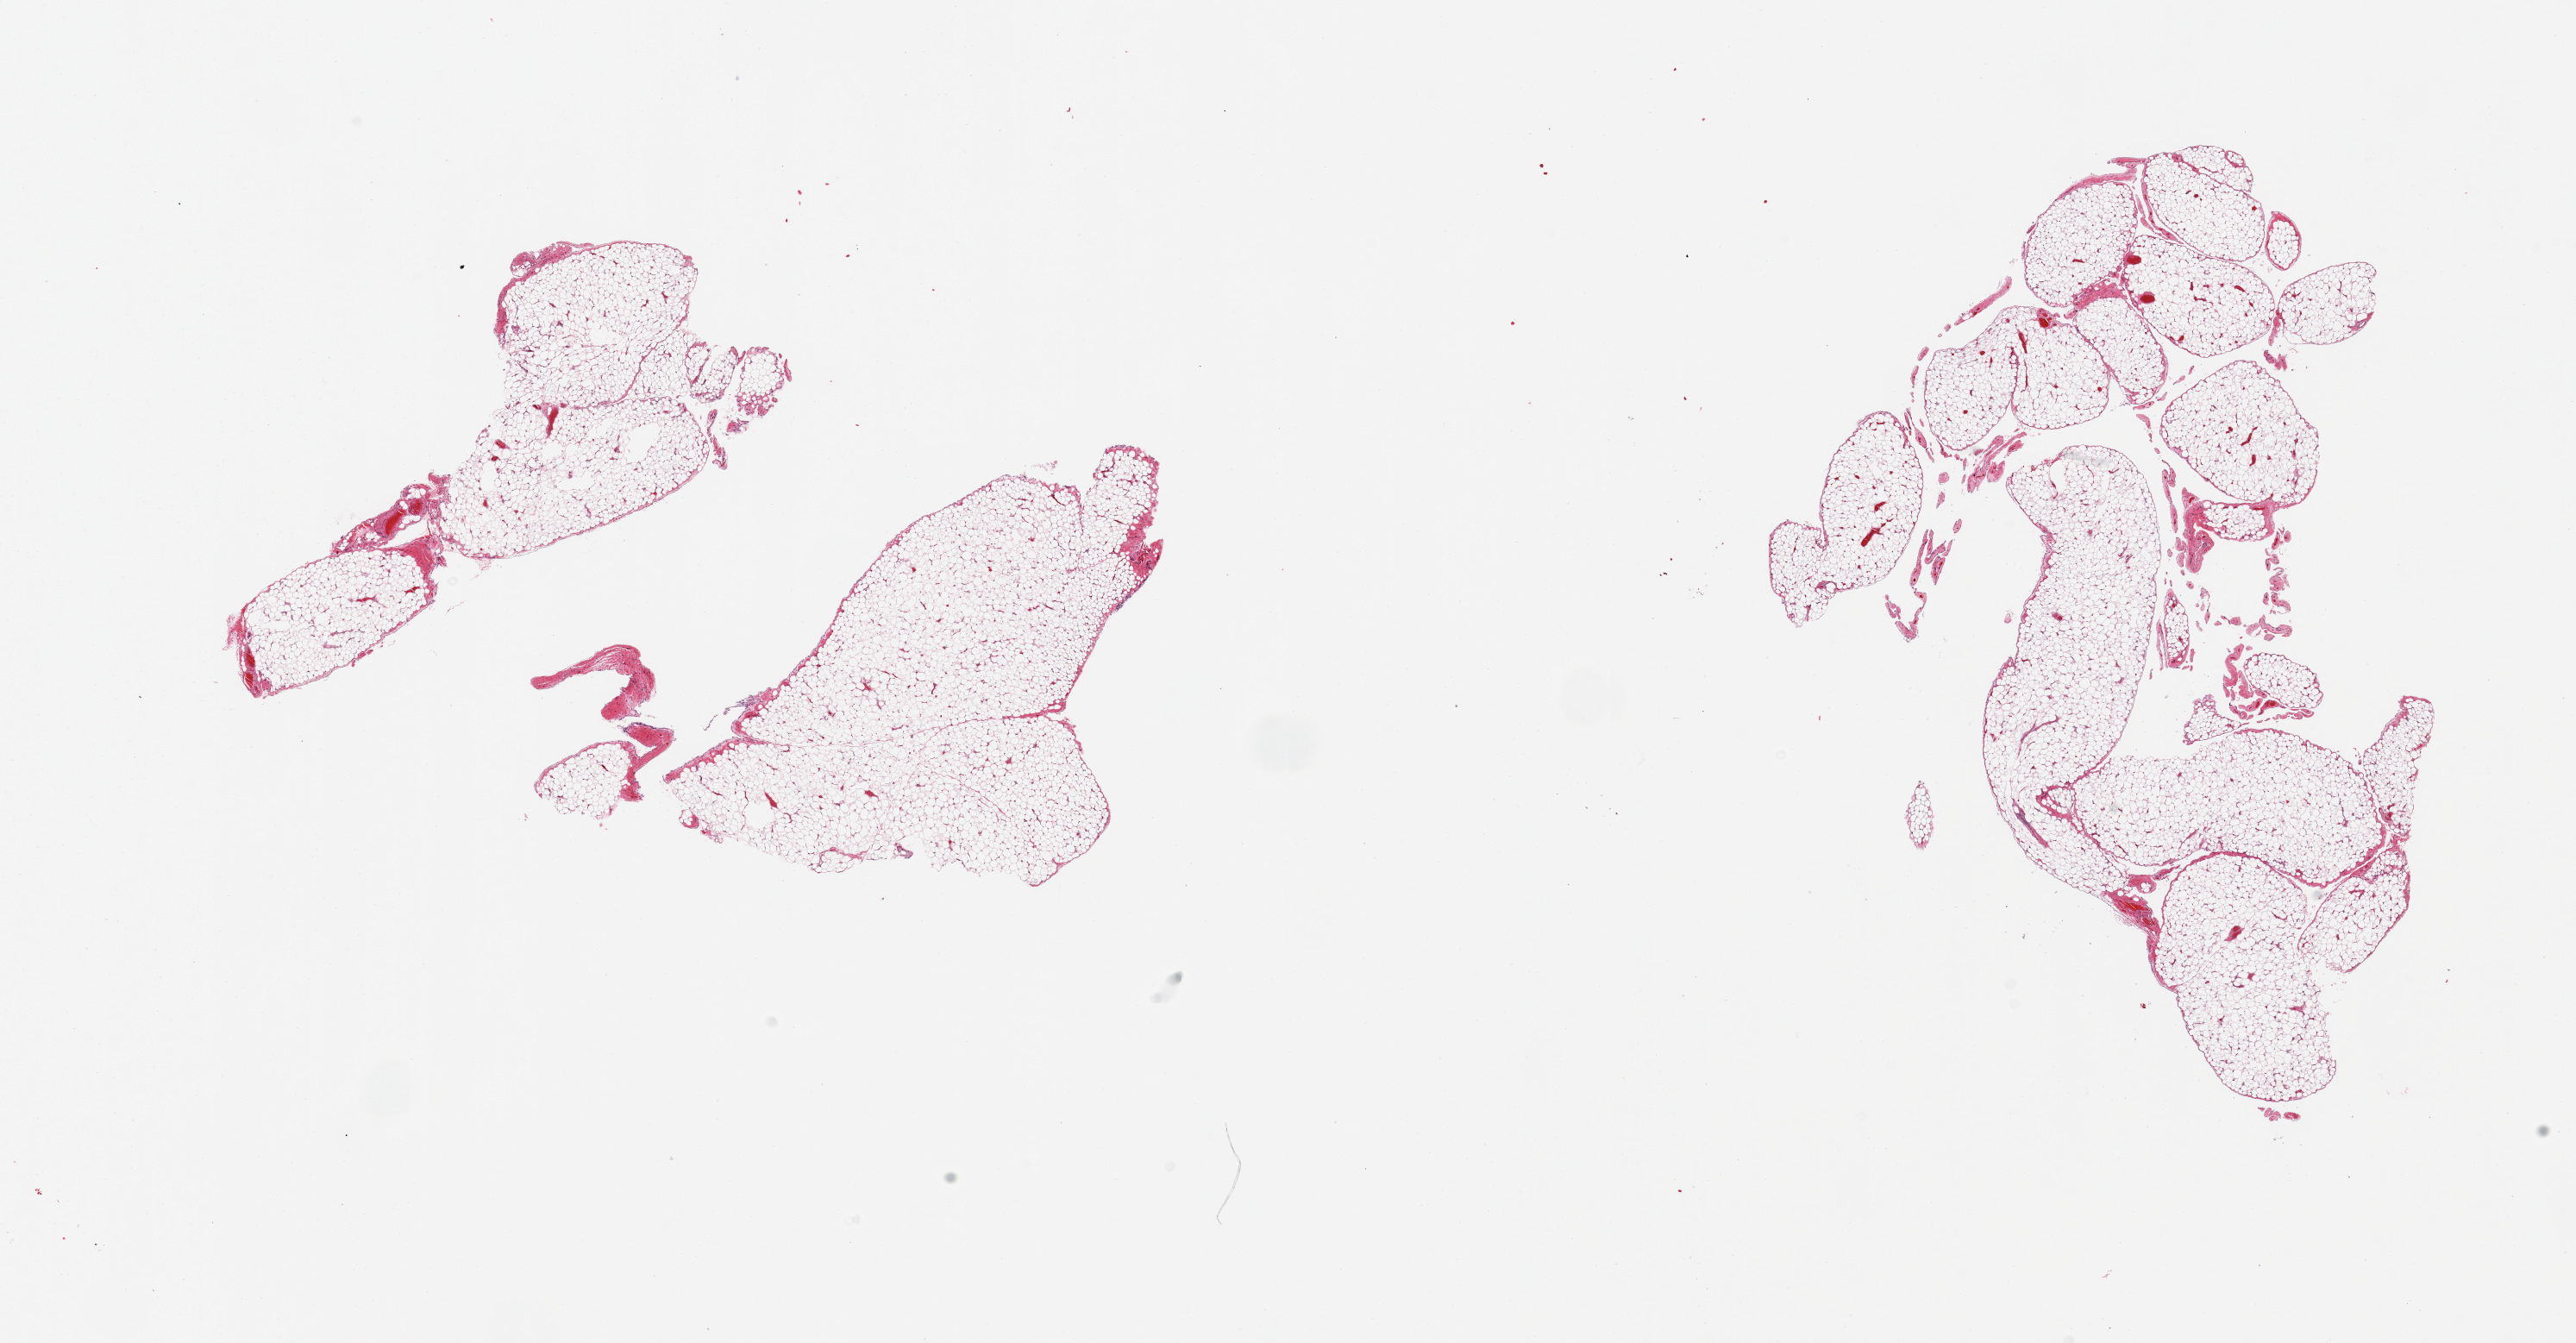
Whole-slide image, H&E stain, brightfield, low-resolution overview of the scanned area, about 23.6 x 12.3 mm (acquisition: 20x scan); PAXgene-fixed paraffin-embedded (PFPE) section; section of omentum (target tissue); tissue donor sample.
* pathologist's review note for this sample: 2 pieces, minimal fascia